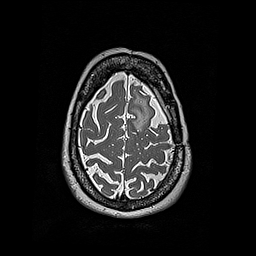
Brain MRI from a brain-tumour surgery series, one axial slice; slice 147 of 192 in the series (ordered by position); 256 × 256 image matrix, field of view 250 × 250 mm. Case-level facts recorded for this patient, not image findings: histopathology: Oligodendroglioma; WHO grade: 2; IDH mutation: yes; tumour location: Left Frontal.
Annotated regions visible in this slice (expert manual segmentation):
- tumour: bounding box [x1, y1, x2, y2] px = [148, 113, 151, 120]